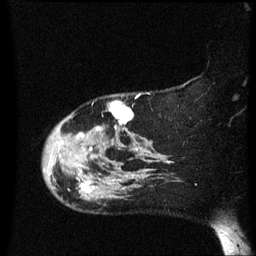
Breast MRI (dynamic contrast-enhanced), one sagittal slice. Dynamic contrast-enhanced series, image 2 of 3 at this slice position (ordered by acquisition). 1.5 T. TE 4.2 ms, TR 8.4 ms. 2.2 mm slice thickness. 256 × 256 image matrix, field of view 200 × 200 mm. Patient: female, 47 years.
Structures marked on this image (semi-automatic segmentation, software-assisted and operator-edited):
- analysis volume of interest (the breast-tissue region the enhancement analysis was run in; not a lesion): bounding box [x1, y1, x2, y2] px = [44, 97, 149, 206]
- tumour enhancement mask (voxels above the 70 % enhancement threshold inside the analysis volume of interest): [76, 102, 141, 194]